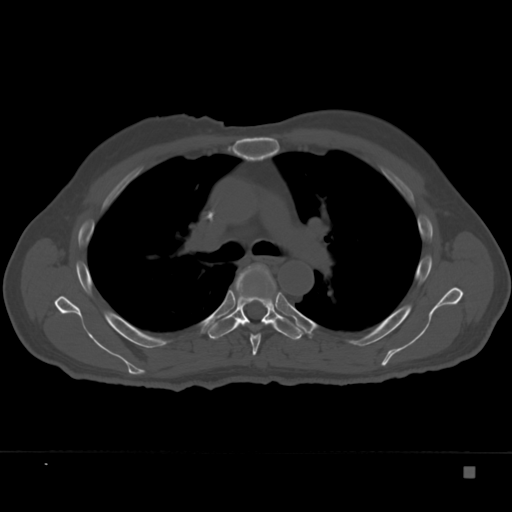
CT including the spine, one axial slice. Position 247 of 332 along the scan axis. Reconstruction kernel Br40s. 120 kVp. Bone window (W 1800 / L 400 HU). 512 × 512 image matrix, field of view 389 × 389 mm. Male patient, age 72 years. Case-level facts recorded for this patient, not image findings: primary cancer: skeletal.
Annotated regions visible in this slice (semi-automatically segmented with operator editing):
- T5 vertebra: bounding box <250,294,278,355> (left, top, right, bottom; pixels)
- T6 vertebra: <207,264,304,340>